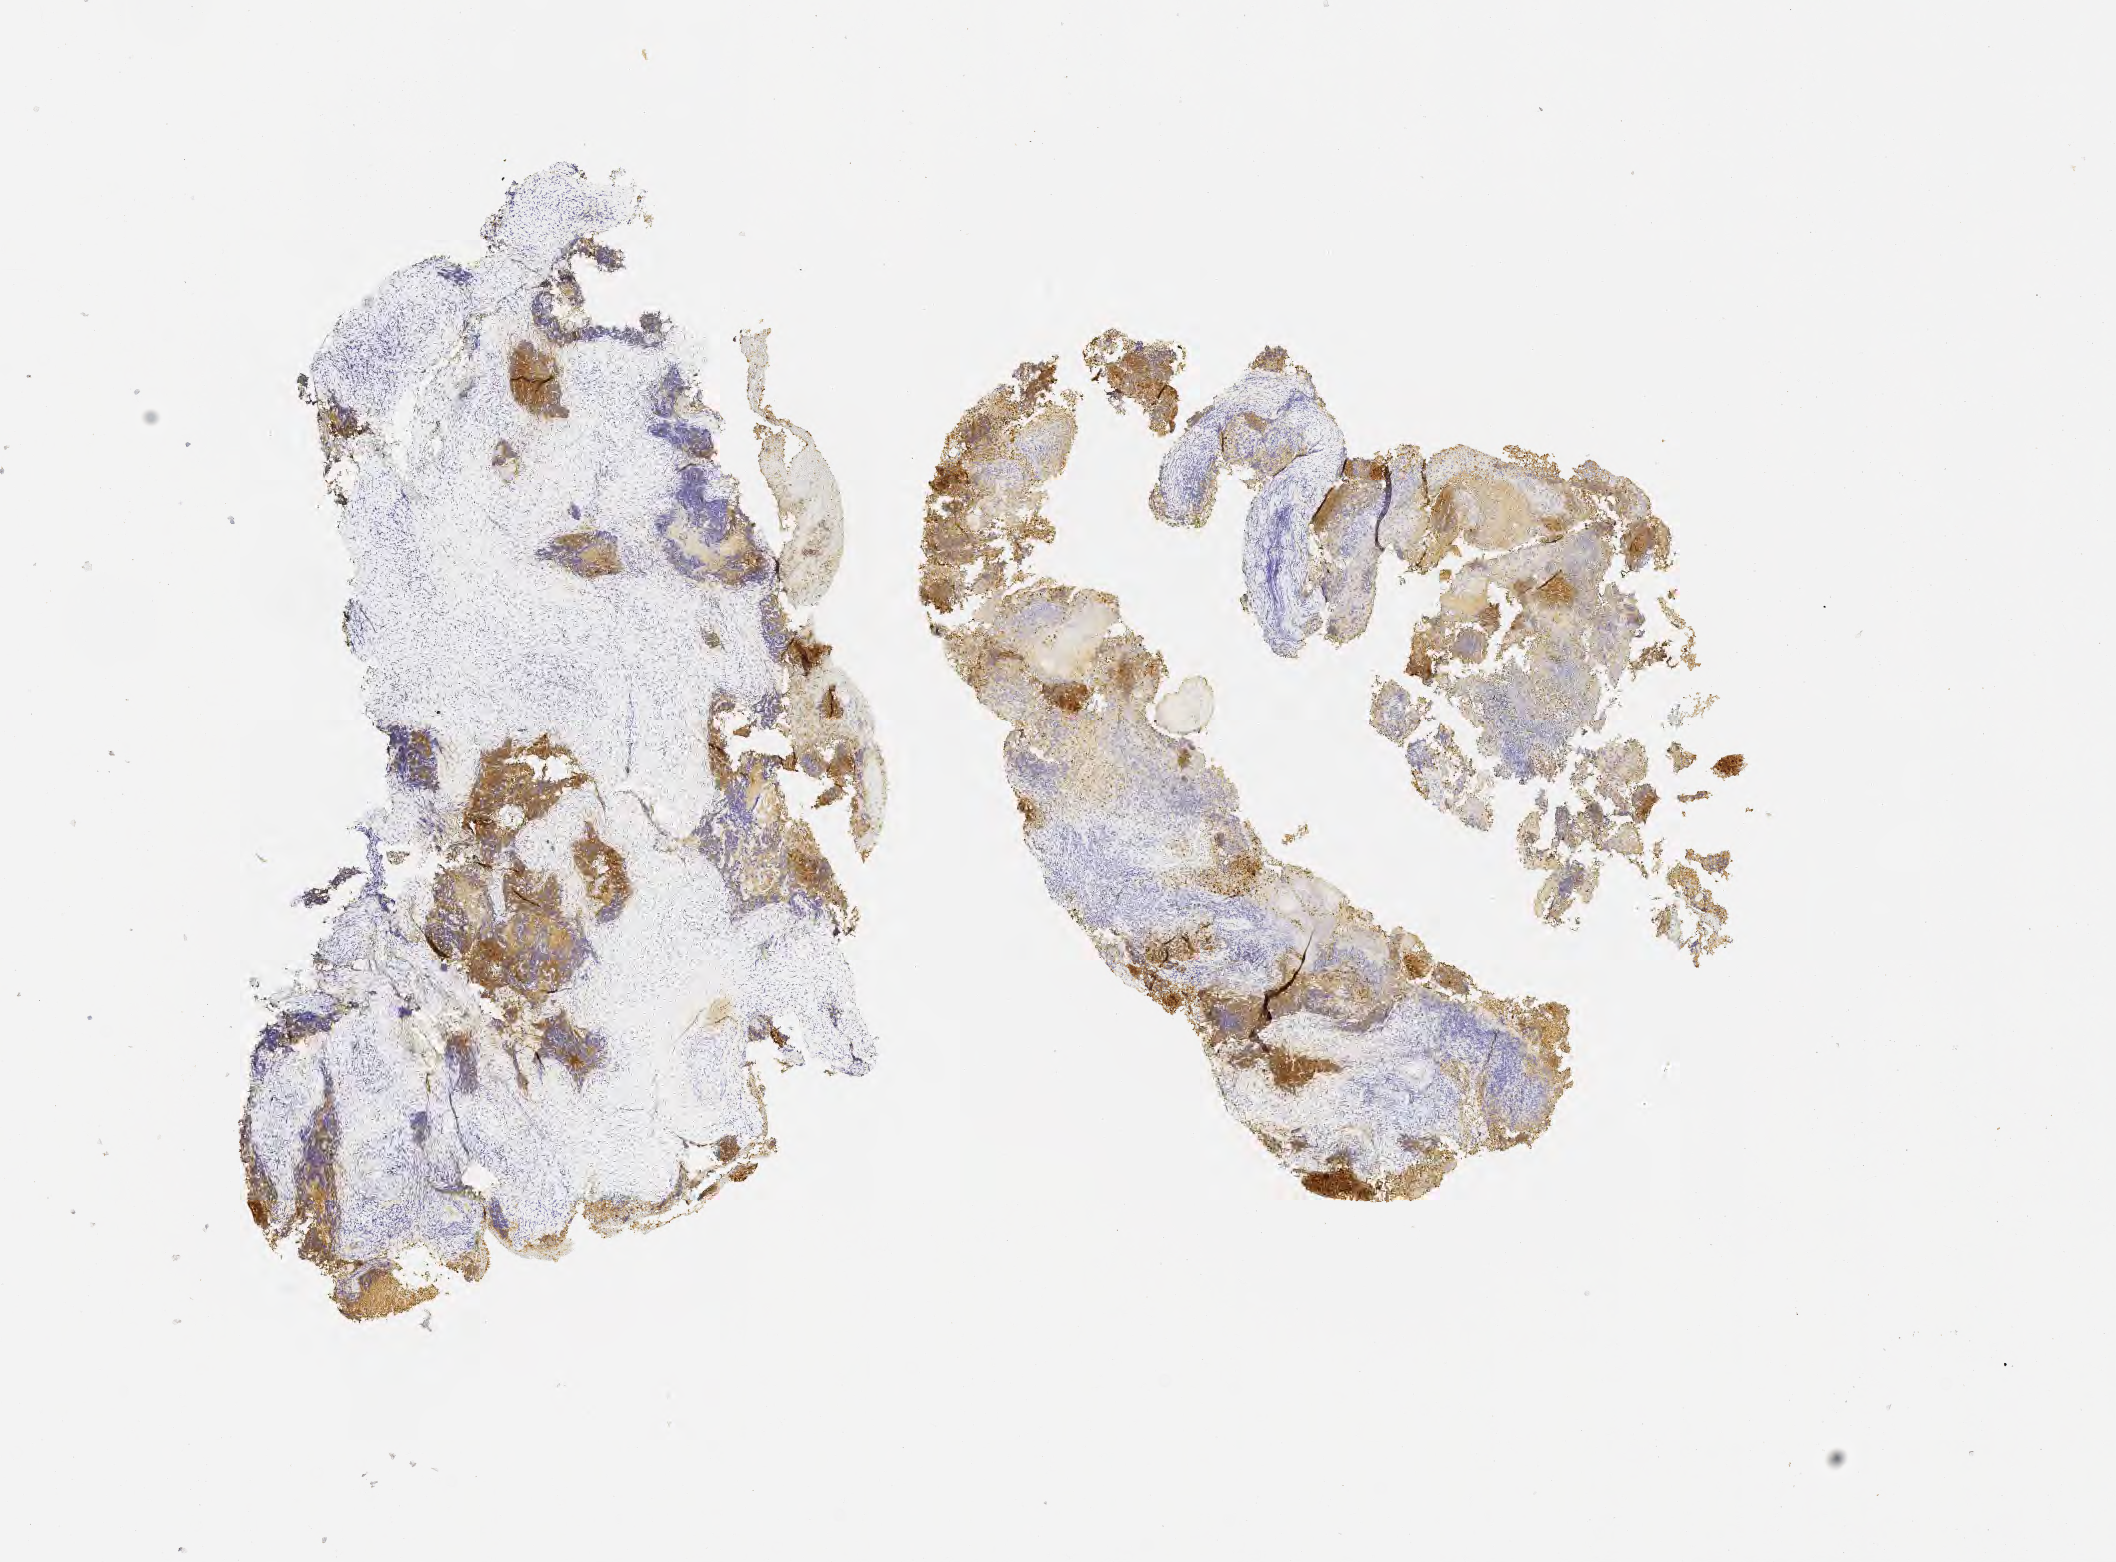
Whole-slide image, immunohistochemical stain for p16 (p16INK4a), low-resolution overview of the scanned area, about 8.6 x 6.3 mm. Specimen: tumor tissue. Anatomic site: cervix. Patient female; aged 47.
Histologic diagnosis: Squamous cell carcinoma, large cell, nonkeratinizing, NOS.